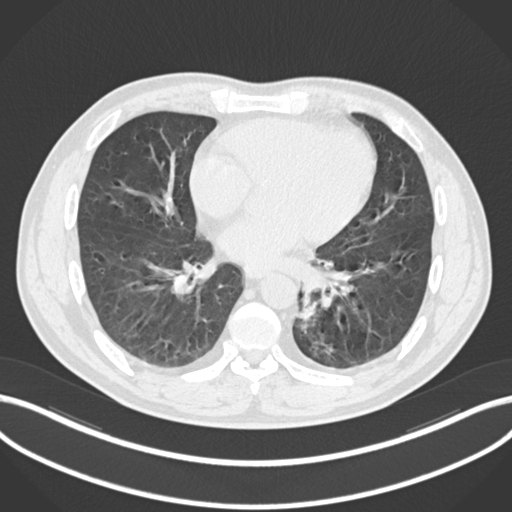
Chest CT, one axial slice. Slice 87 of 223 in the series (ordered by position). 120 kVp. Lung window (W 1500 / L -600 HU). 1 mm slice thickness. 512 × 512 image matrix, field of view 400 × 400 mm. Male patient, age 50 years. Case-level facts recorded for this patient, not image findings: clinical TNM (as recorded): T2a N3 M0.
Annotated regions visible in this slice (bounding box drawn by a radiologist):
- lung tumour (recorded histology: squamous cell carcinoma): bounding box (x1, y1, x2, y2) in pixels: (297, 290, 322, 334)